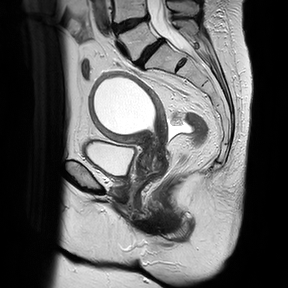
Pelvic MRI for cervical cancer, one sagittal slice. Slice 15 of 30 in the series (ordered by position). T2-weighted. 1.5 T. TE 100 ms, TR 4816.3 ms. 288 × 288 image matrix, field of view 300 × 300 mm. Patient: female, 74 years.
Outlined on this slice (expert manual segmentation):
- uterus and cervix: box from (x=87, y=71) to (x=168, y=182) px